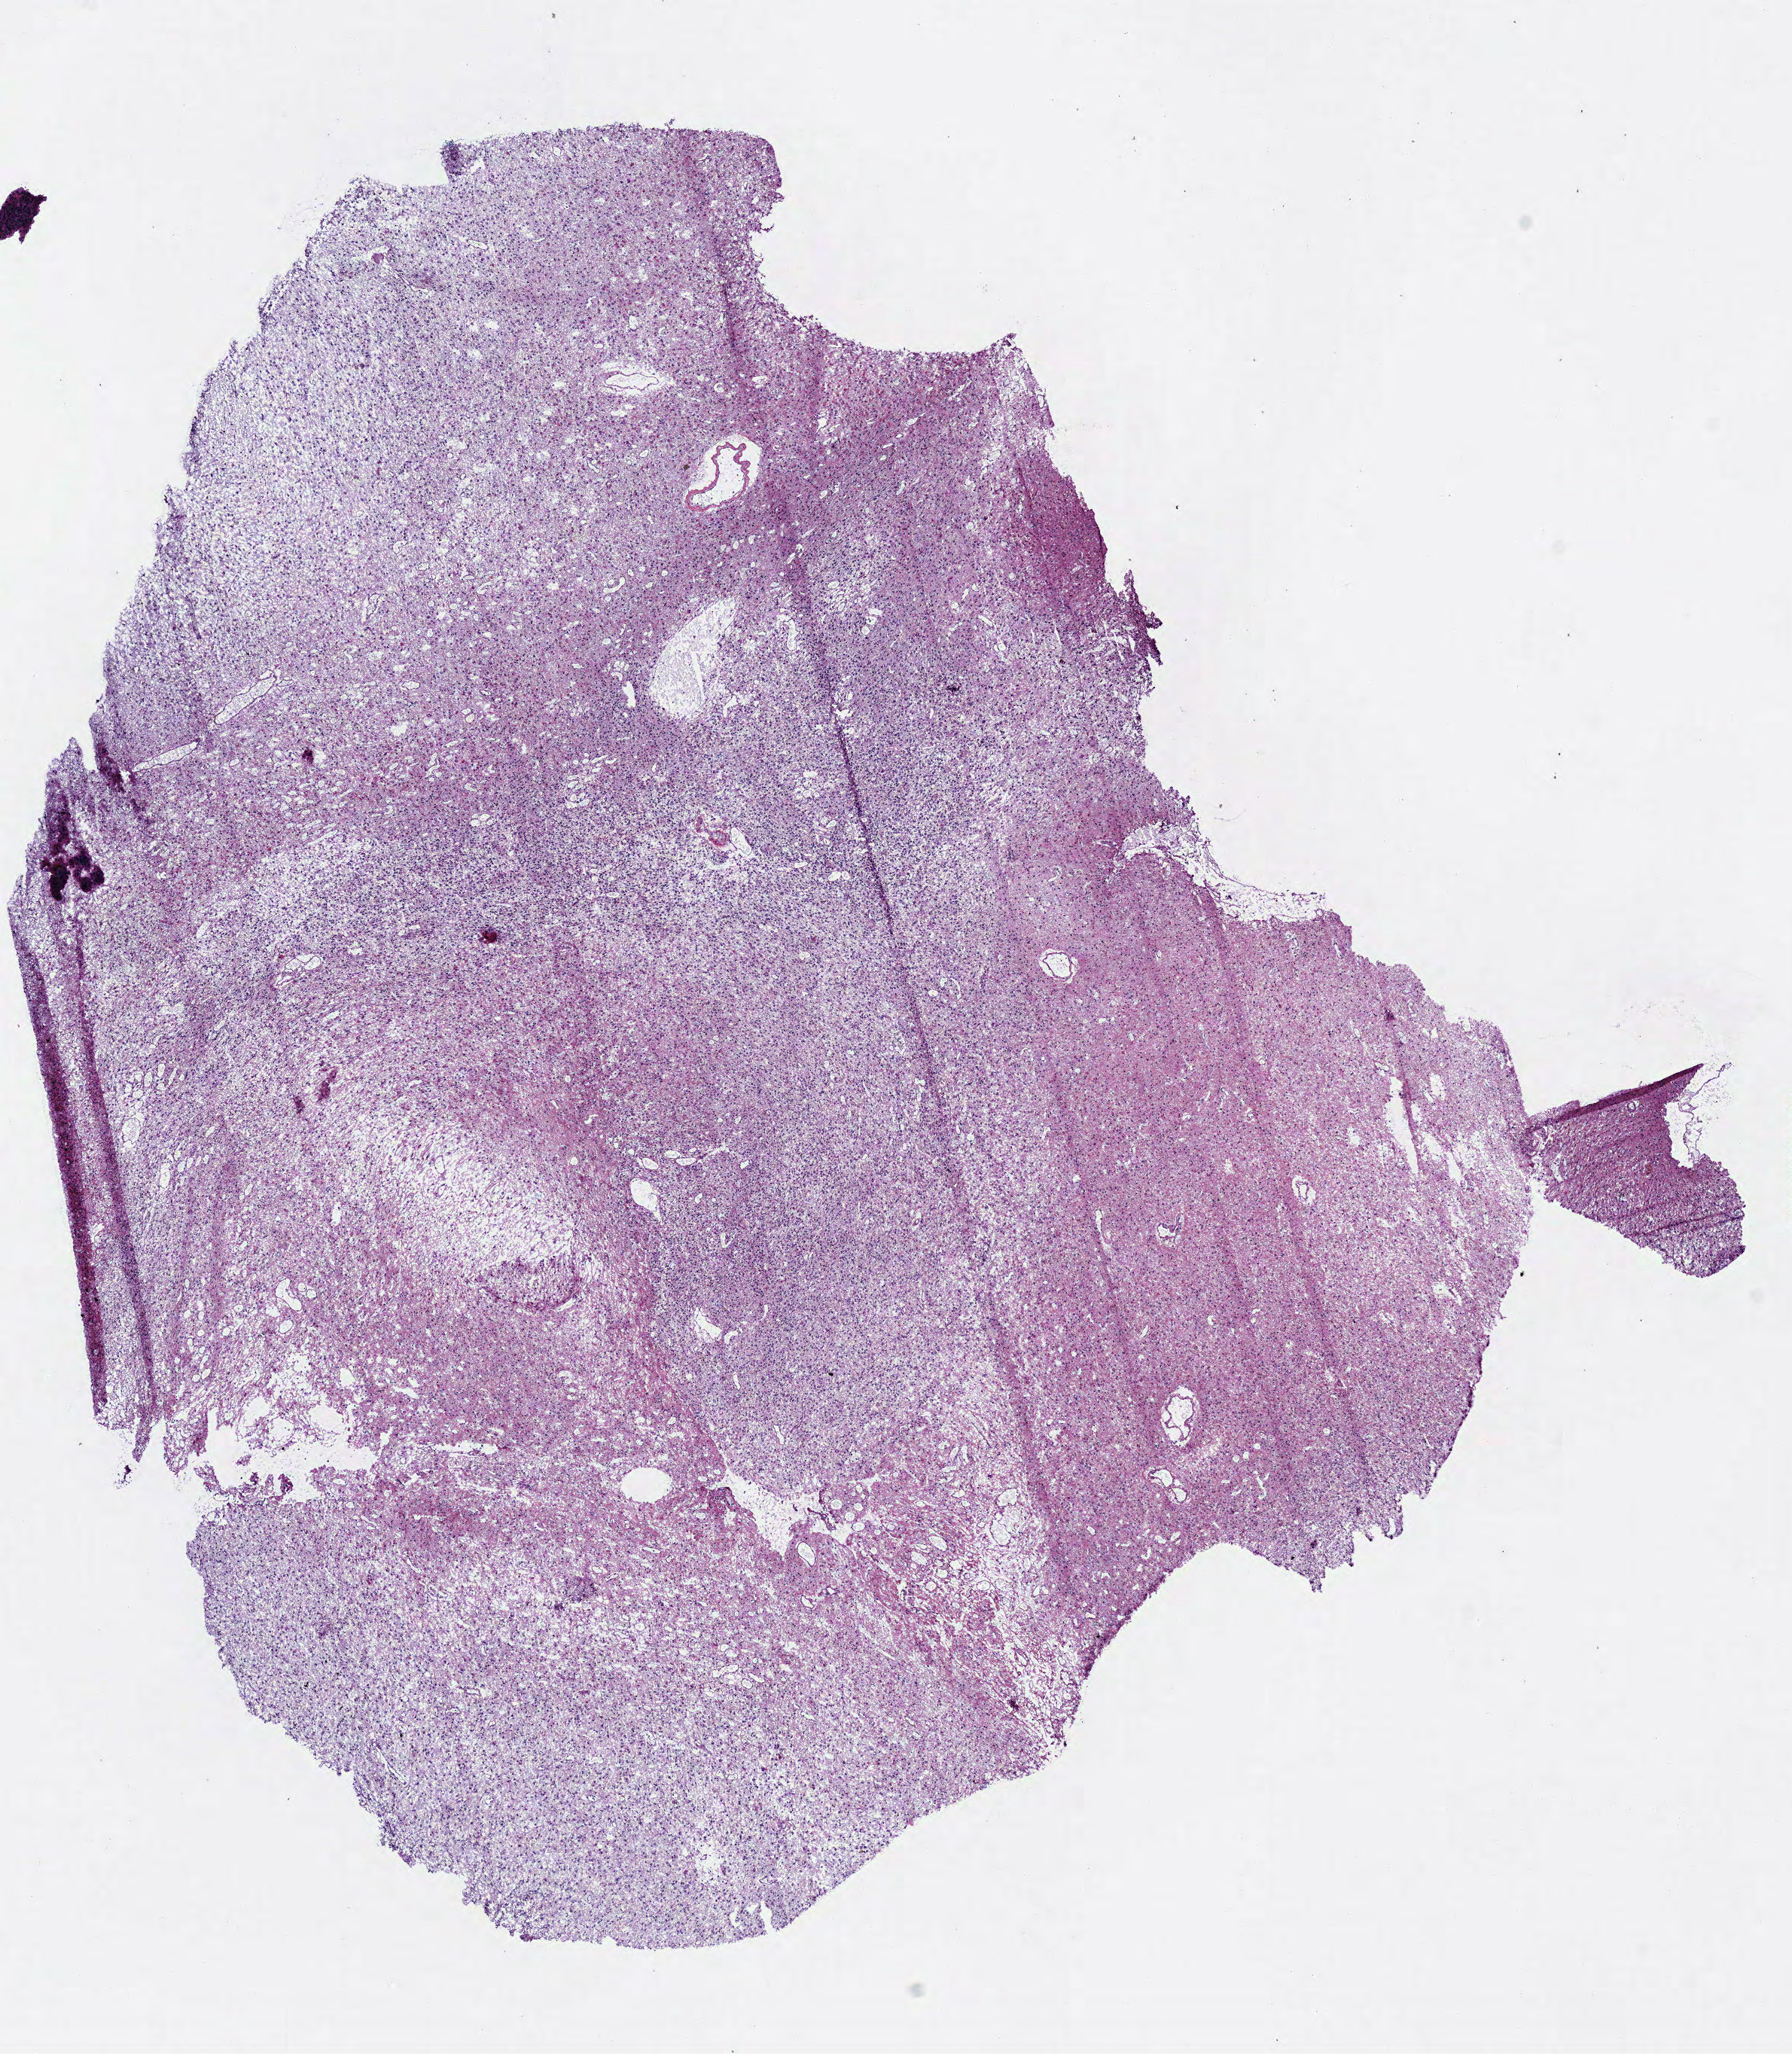
Digitized H&E-stained tissue section (whole slide) — low-resolution overview of the scanned area, about 9.4 x 10.7 mm (from a 40x scan); frozen section from the bottom of the tissue portion; sample: primary tumour, brain. Patient: female, age at initial diagnosis 43 years. Histologic grade: G2 (moderately differentiated). Pathologist review of this section (percent, as recorded): tumour cells 100%, tumour nuclei 75%, normal cells 0%, stromal cells 0%, necrosis 0%.
Laterality: left. Pathologic diagnosis: Mixed glioma.